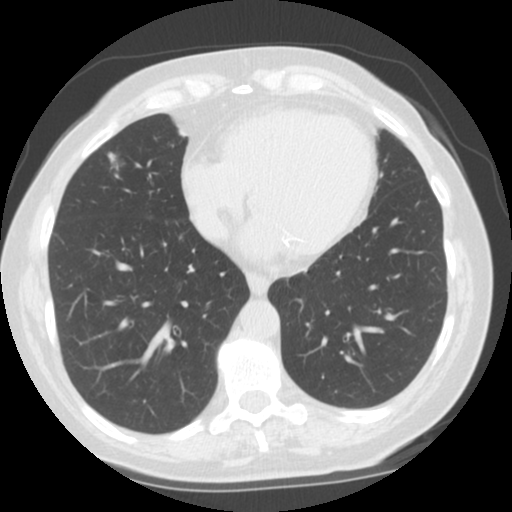
Axial slice from a low-dose chest CT screening exam; first (baseline) screen; lung window (W 1500 / L -600 HU); 140 kVp; 512 × 512 image matrix, field of view 300 × 300 mm. Female participant, aged 71 years at enrolment. Current smoker at enrolment.
Expert-annotated lung lesion, bounding box <83,141,140,192> (left, top, right, bottom; pixels). The screening reader recorded 2 non-calcified nodules or masses ≥4 mm on this exam; which of them this box marks is not recorded. Official screen result: positive, change unspecified: nodule(s) >= 4 mm or enlarging nodule(s), mass(es), or other non-specific abnormalities suspicious for lung cancer. Participant outcome: lung cancer diagnosed 491 days after this screen (after the second annual screen) — adenocarcinoma, NOS, right middle lobe, moderately differentiated (G2), stage IA (AJCC 6th edition), 12 mm at pathology.